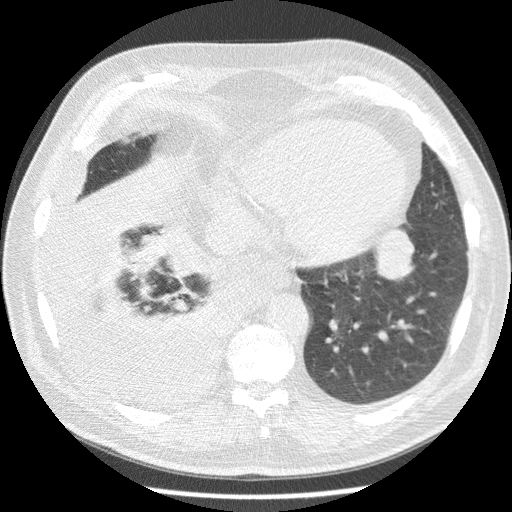
Low-dose screening chest CT, one axial slice; slice 60 of 180 in the series (ordered by position); lung window (W 1500 / L -600 HU); 512 × 512 image matrix.
Outlined on this slice (outlined manually by an expert reader):
- lesion 1 (tumor, lower lobe of left lung): bounding box (x1, y1, x2, y2) in pixels: (375, 228, 414, 280)